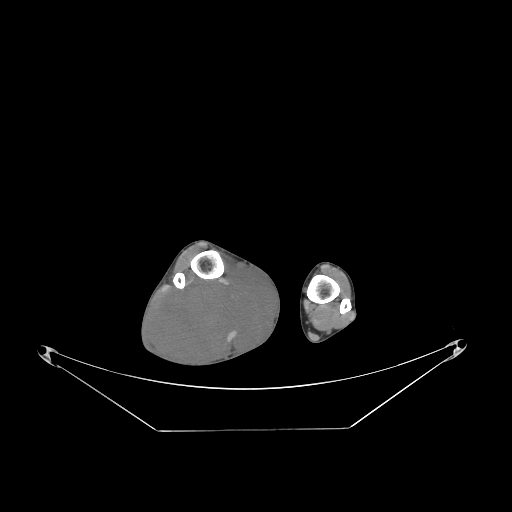
CT of an extremity soft-tissue mass (from a PET/CT study), one axial slice; slice 59 of 267 in the series (ordered by position); reconstruction kernel STANDARD; 140 kVp; soft-tissue window (W 400 / L 40 HU); 3.75 mm slice thickness; 512 × 512 image matrix. Male patient. From the clinical record (not read from this slice): histological type: liposarcoma - round cell; grade: high; site of the primary tumour: right calf.
Structures marked on this image (expert contour drawn on MRI and transferred to this co-registered scan by the dataset authors):
- gross tumour volume (mass): bounding box (x1, y1, x2, y2) in pixels: (151, 267, 277, 368)